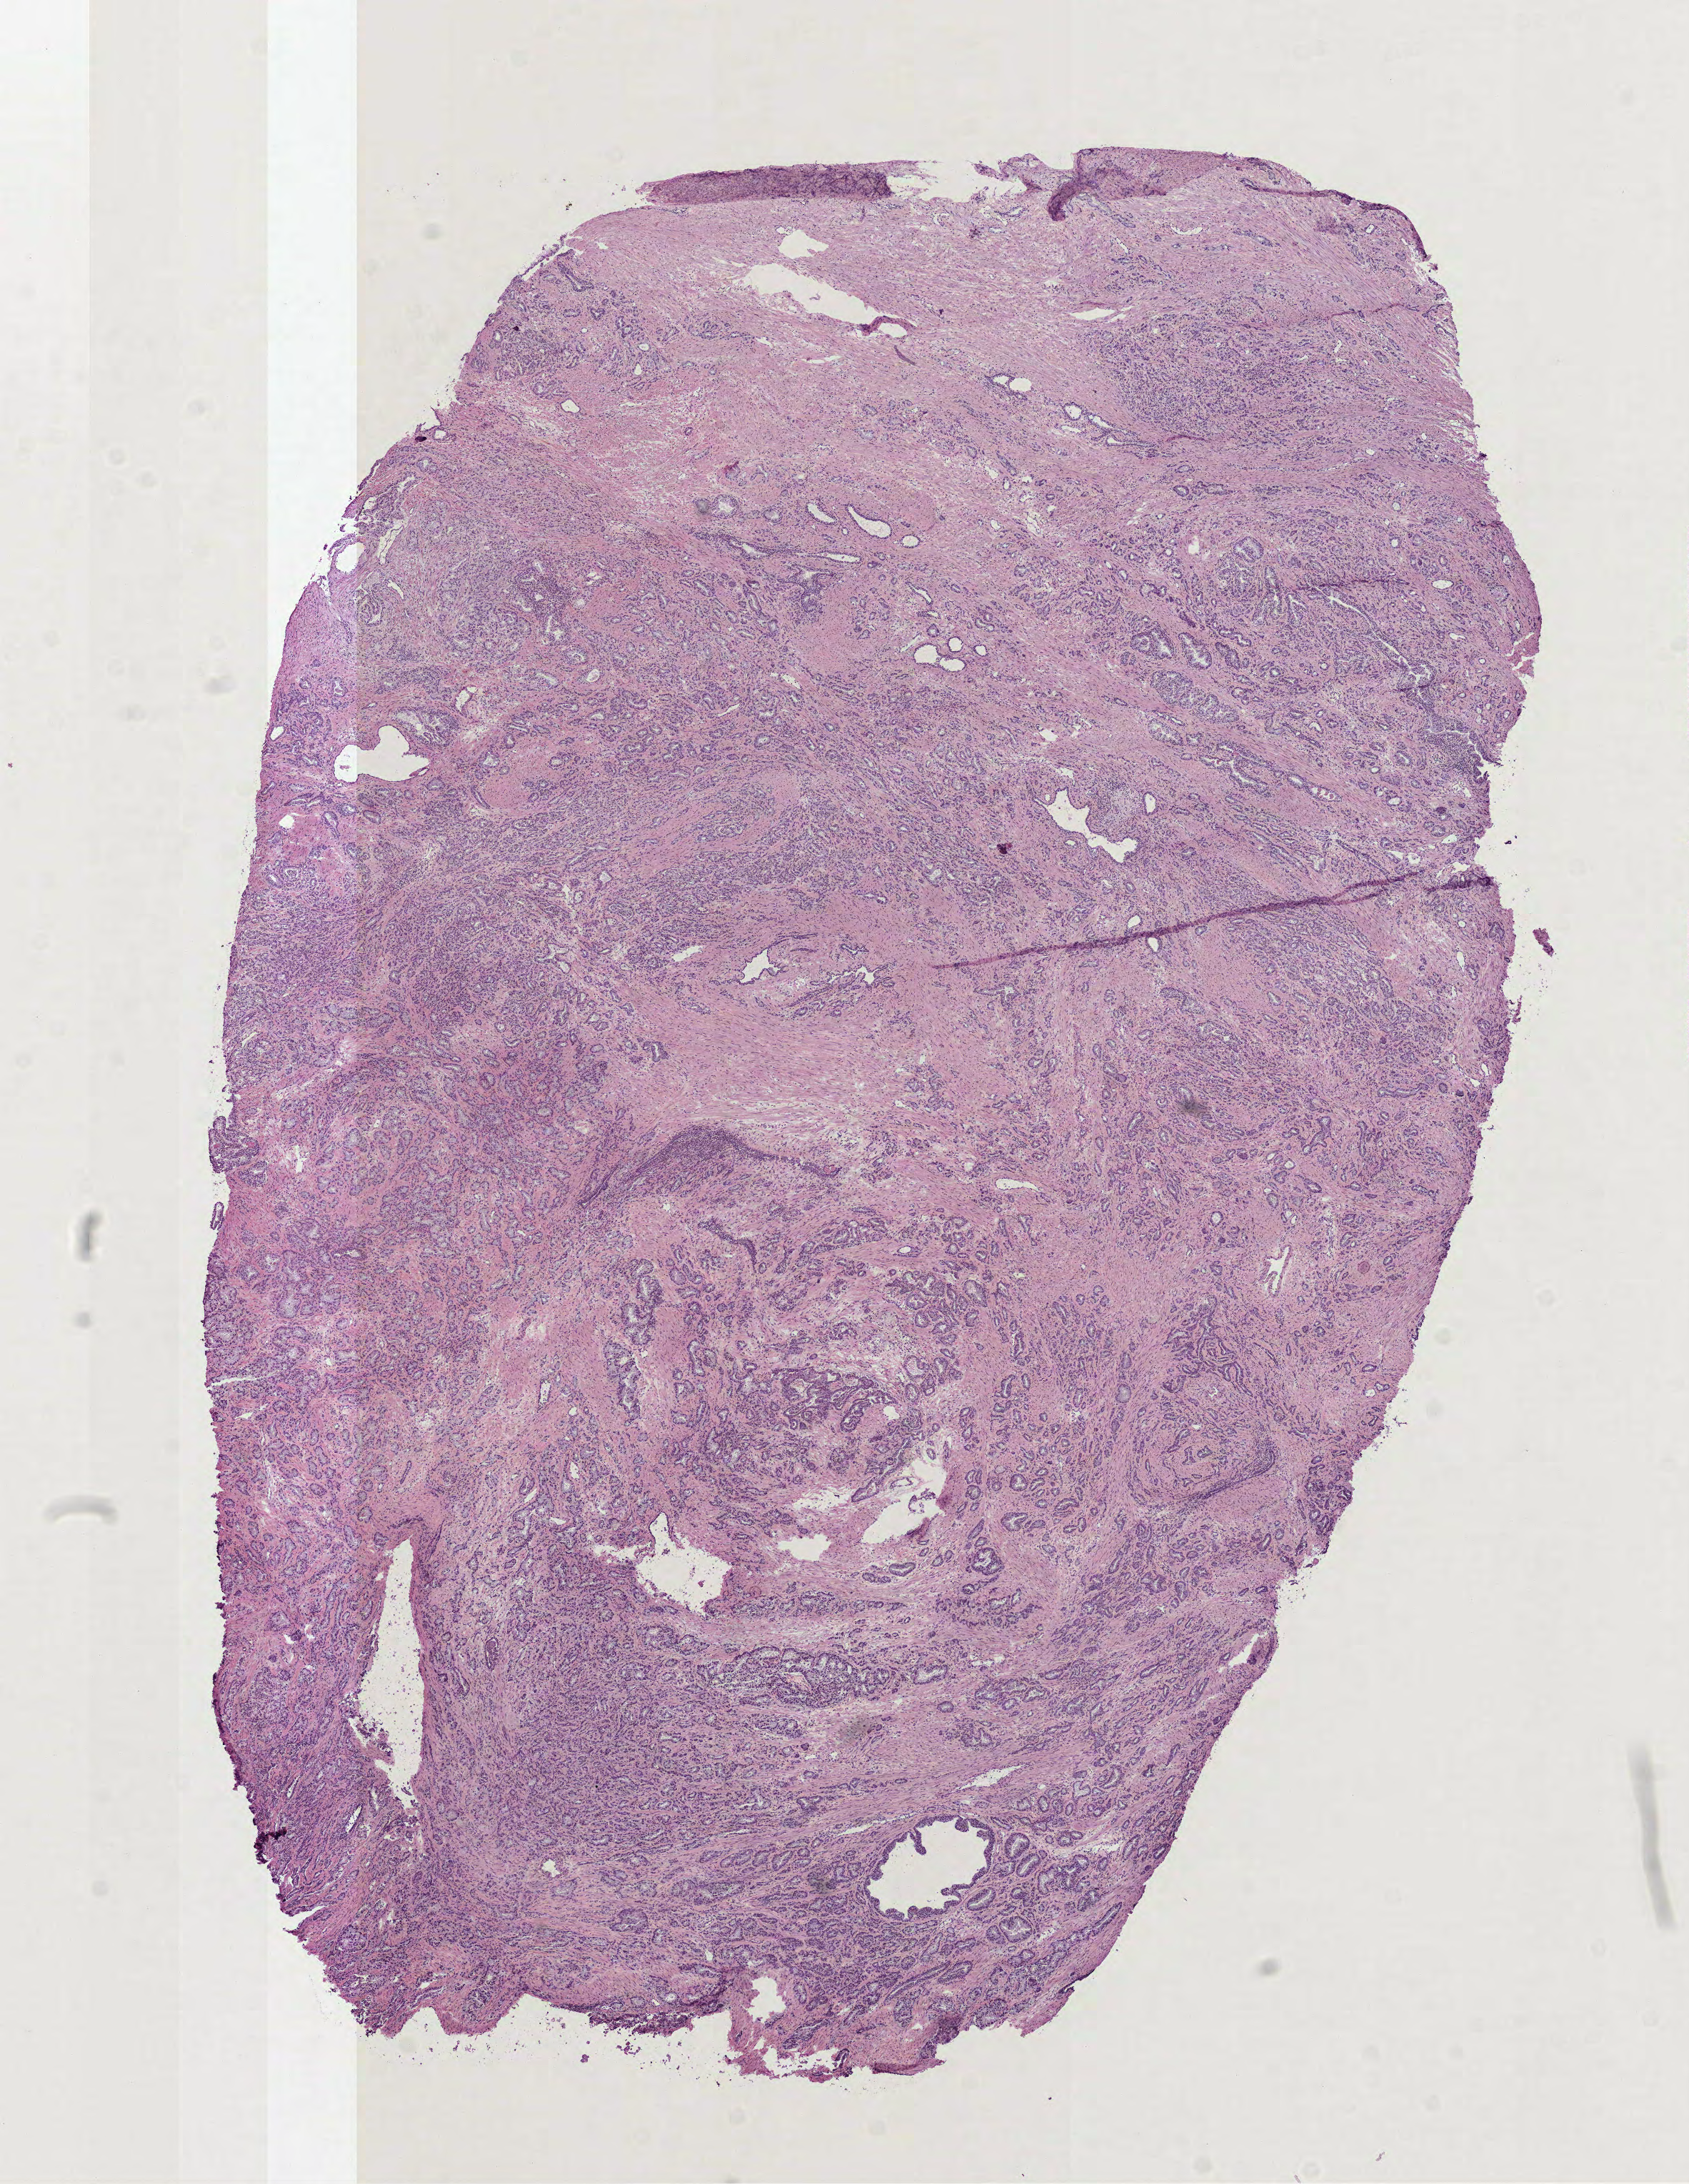
H&E-stained whole-slide image, low-resolution overview of the scanned area, about 9.5 x 12.3 mm; frozen section from the top of the tissue portion; prostate, primary tumour sample. Patient: male, age at initial diagnosis 66 years. Gleason score: 7 (4+3). Pathologist review of this section (percent, as recorded): tumour cells 70%, tumour nuclei 70%, normal cells 10%, stromal cells 20%, necrosis 0%. Inflammatory infiltration, as recorded: lymphocyte infiltration 5%, monocyte infiltration 0%, neutrophil infiltration 0%.
* histologic diagnosis: Acinar cell carcinoma (prostate gland)
* lymph nodes positive (case pathology): 0 of 2 examined